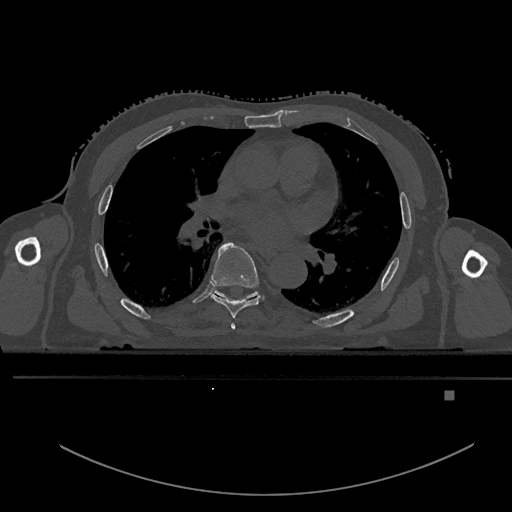
CT including the spine, one axial slice. Position 297 of 969 along the scan axis. Bone window (W 1800 / L 400 HU). 0.5 mm slice thickness. 512 × 512 image matrix, field of view 456 × 456 mm. Patient: male, 82 years. From the clinical record (not read from this slice): primary cancer: prostate.
Structures marked on this image (semi-automatically segmented with operator editing):
- T5 vertebra: bounding box [x1, y1, x2, y2] px = [231, 323, 236, 330]
- T6 vertebra: [211, 242, 260, 318]
- T7 vertebra: [215, 291, 256, 298]